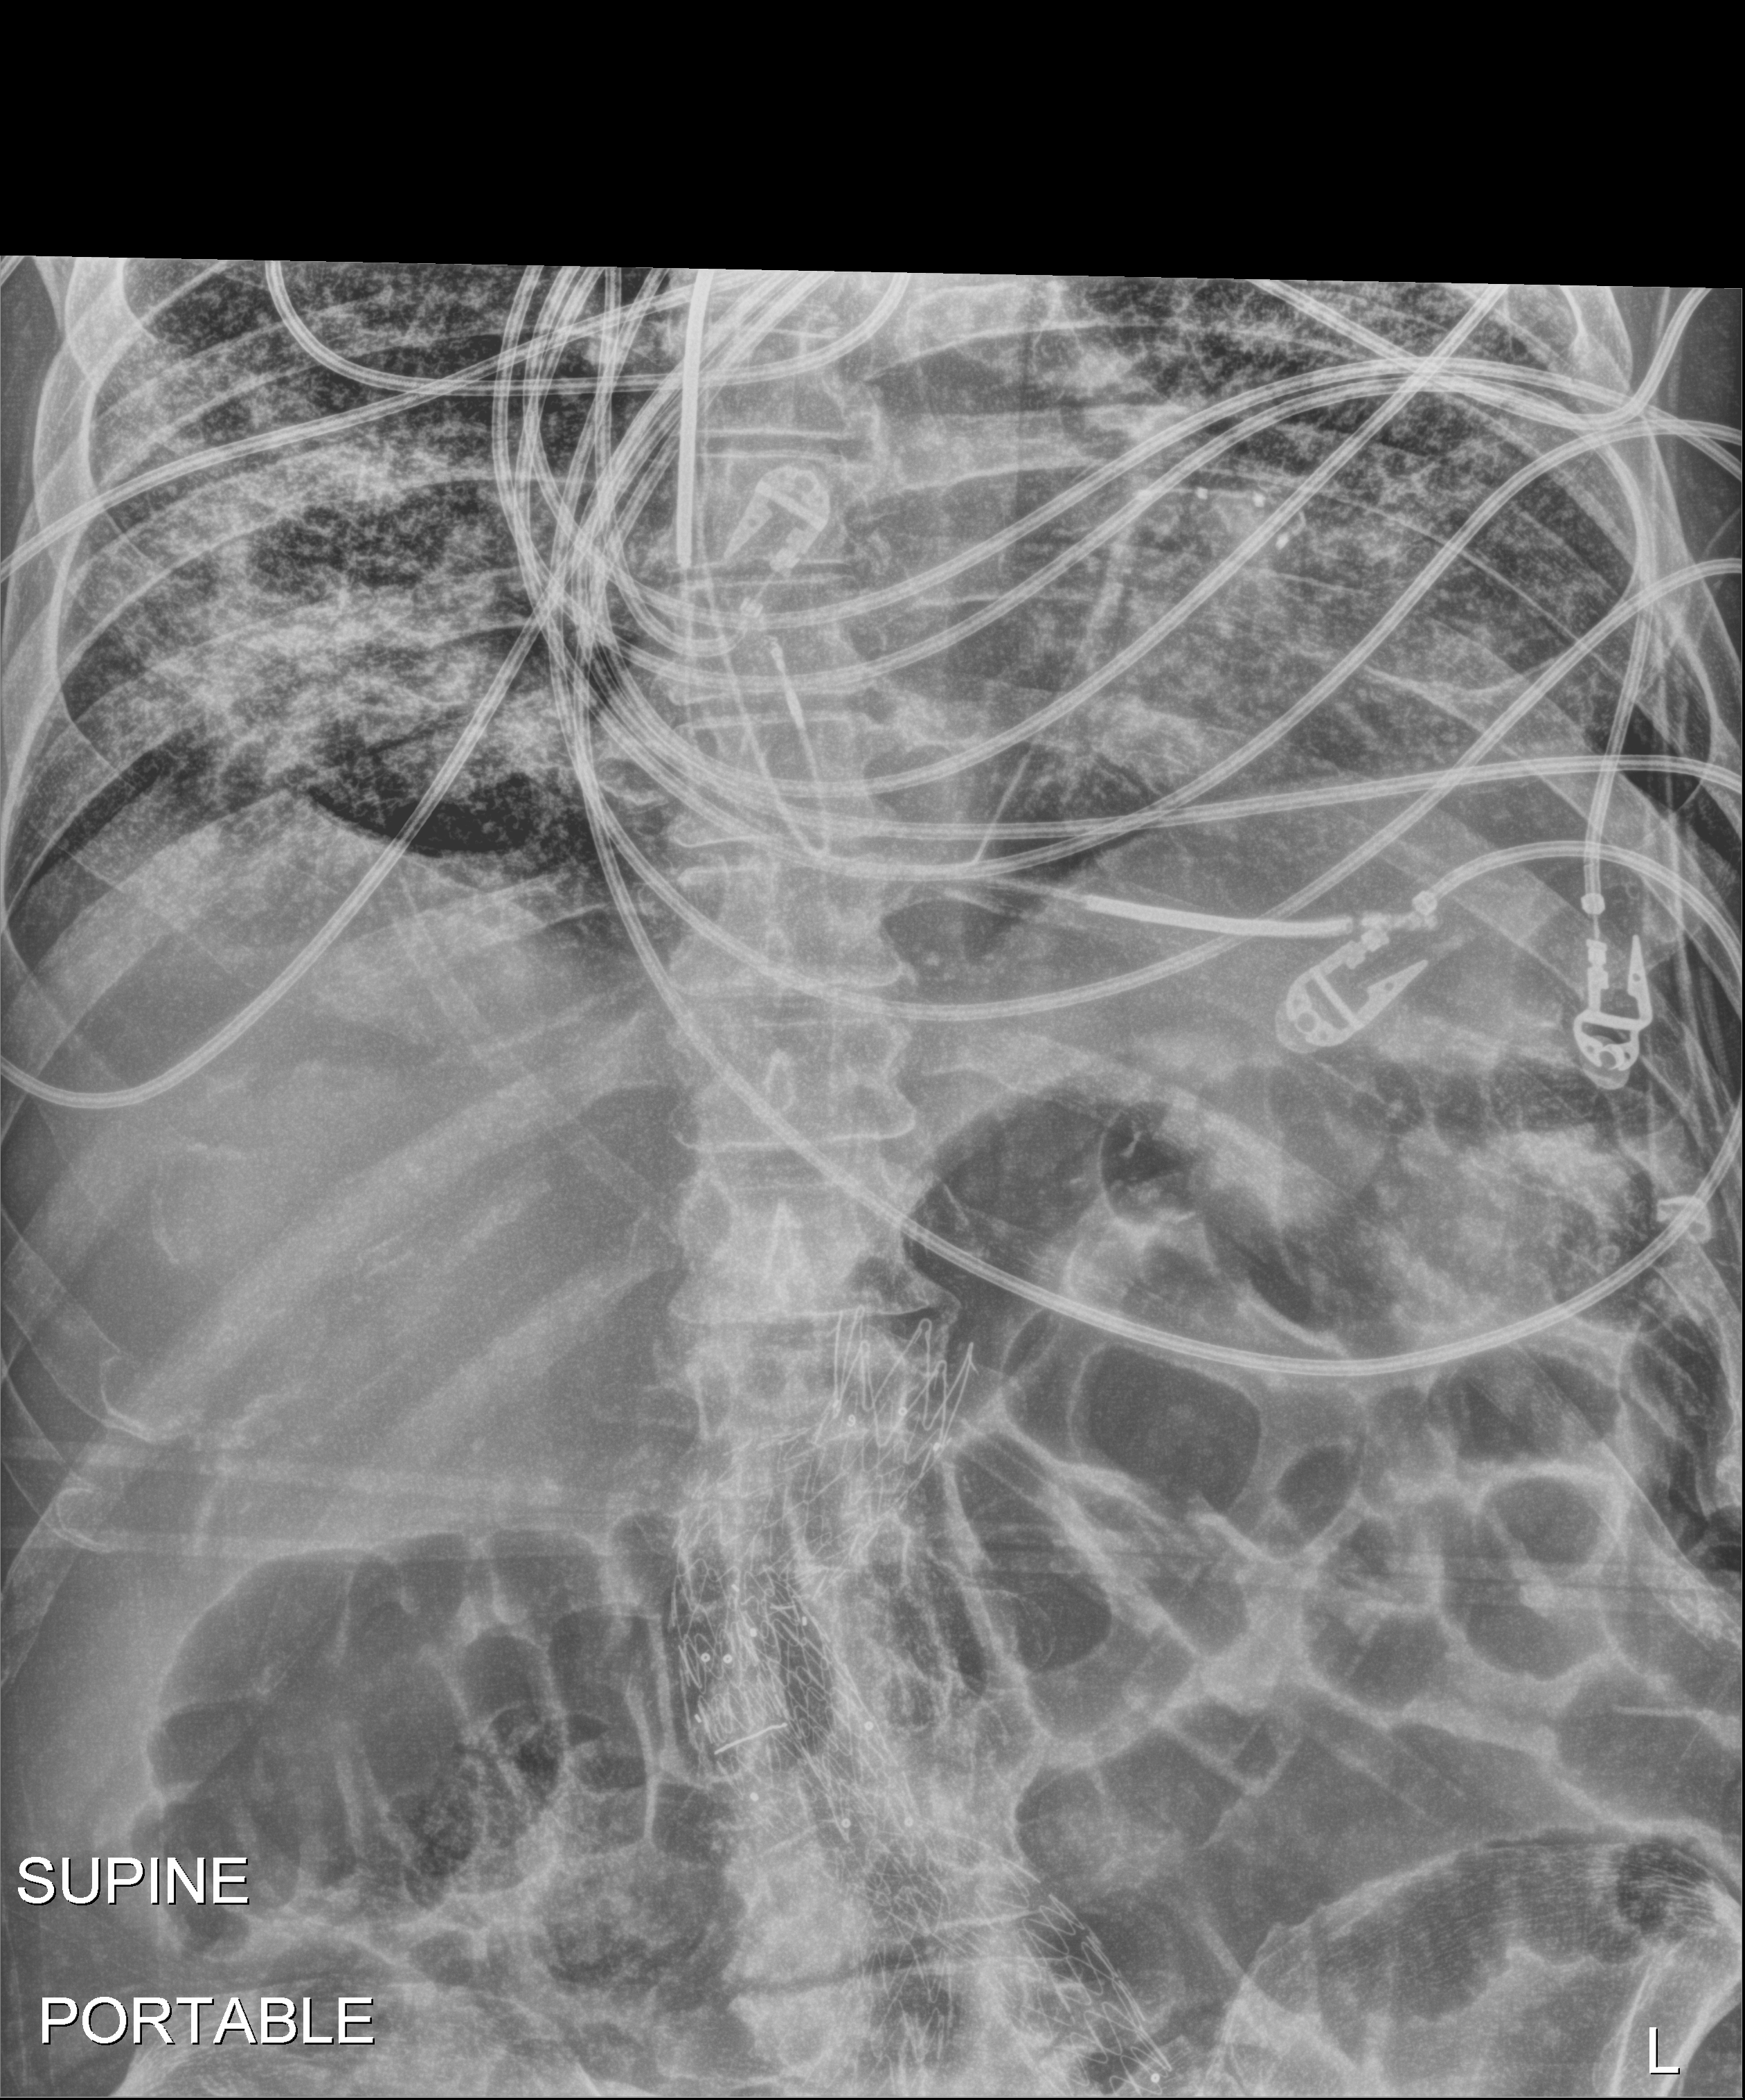
Abdomen radiograph, anteroposterior (AP) projection. Patient hospitalised with COVID-19; male, aged 60–74 years.
From the hospital-stay record, not from the radiograph (when in the stay this image was taken is not recorded): diabetes (admission record): yes; mechanically ventilated during this hospital stay: yes; length of hospital stay: 36 days.